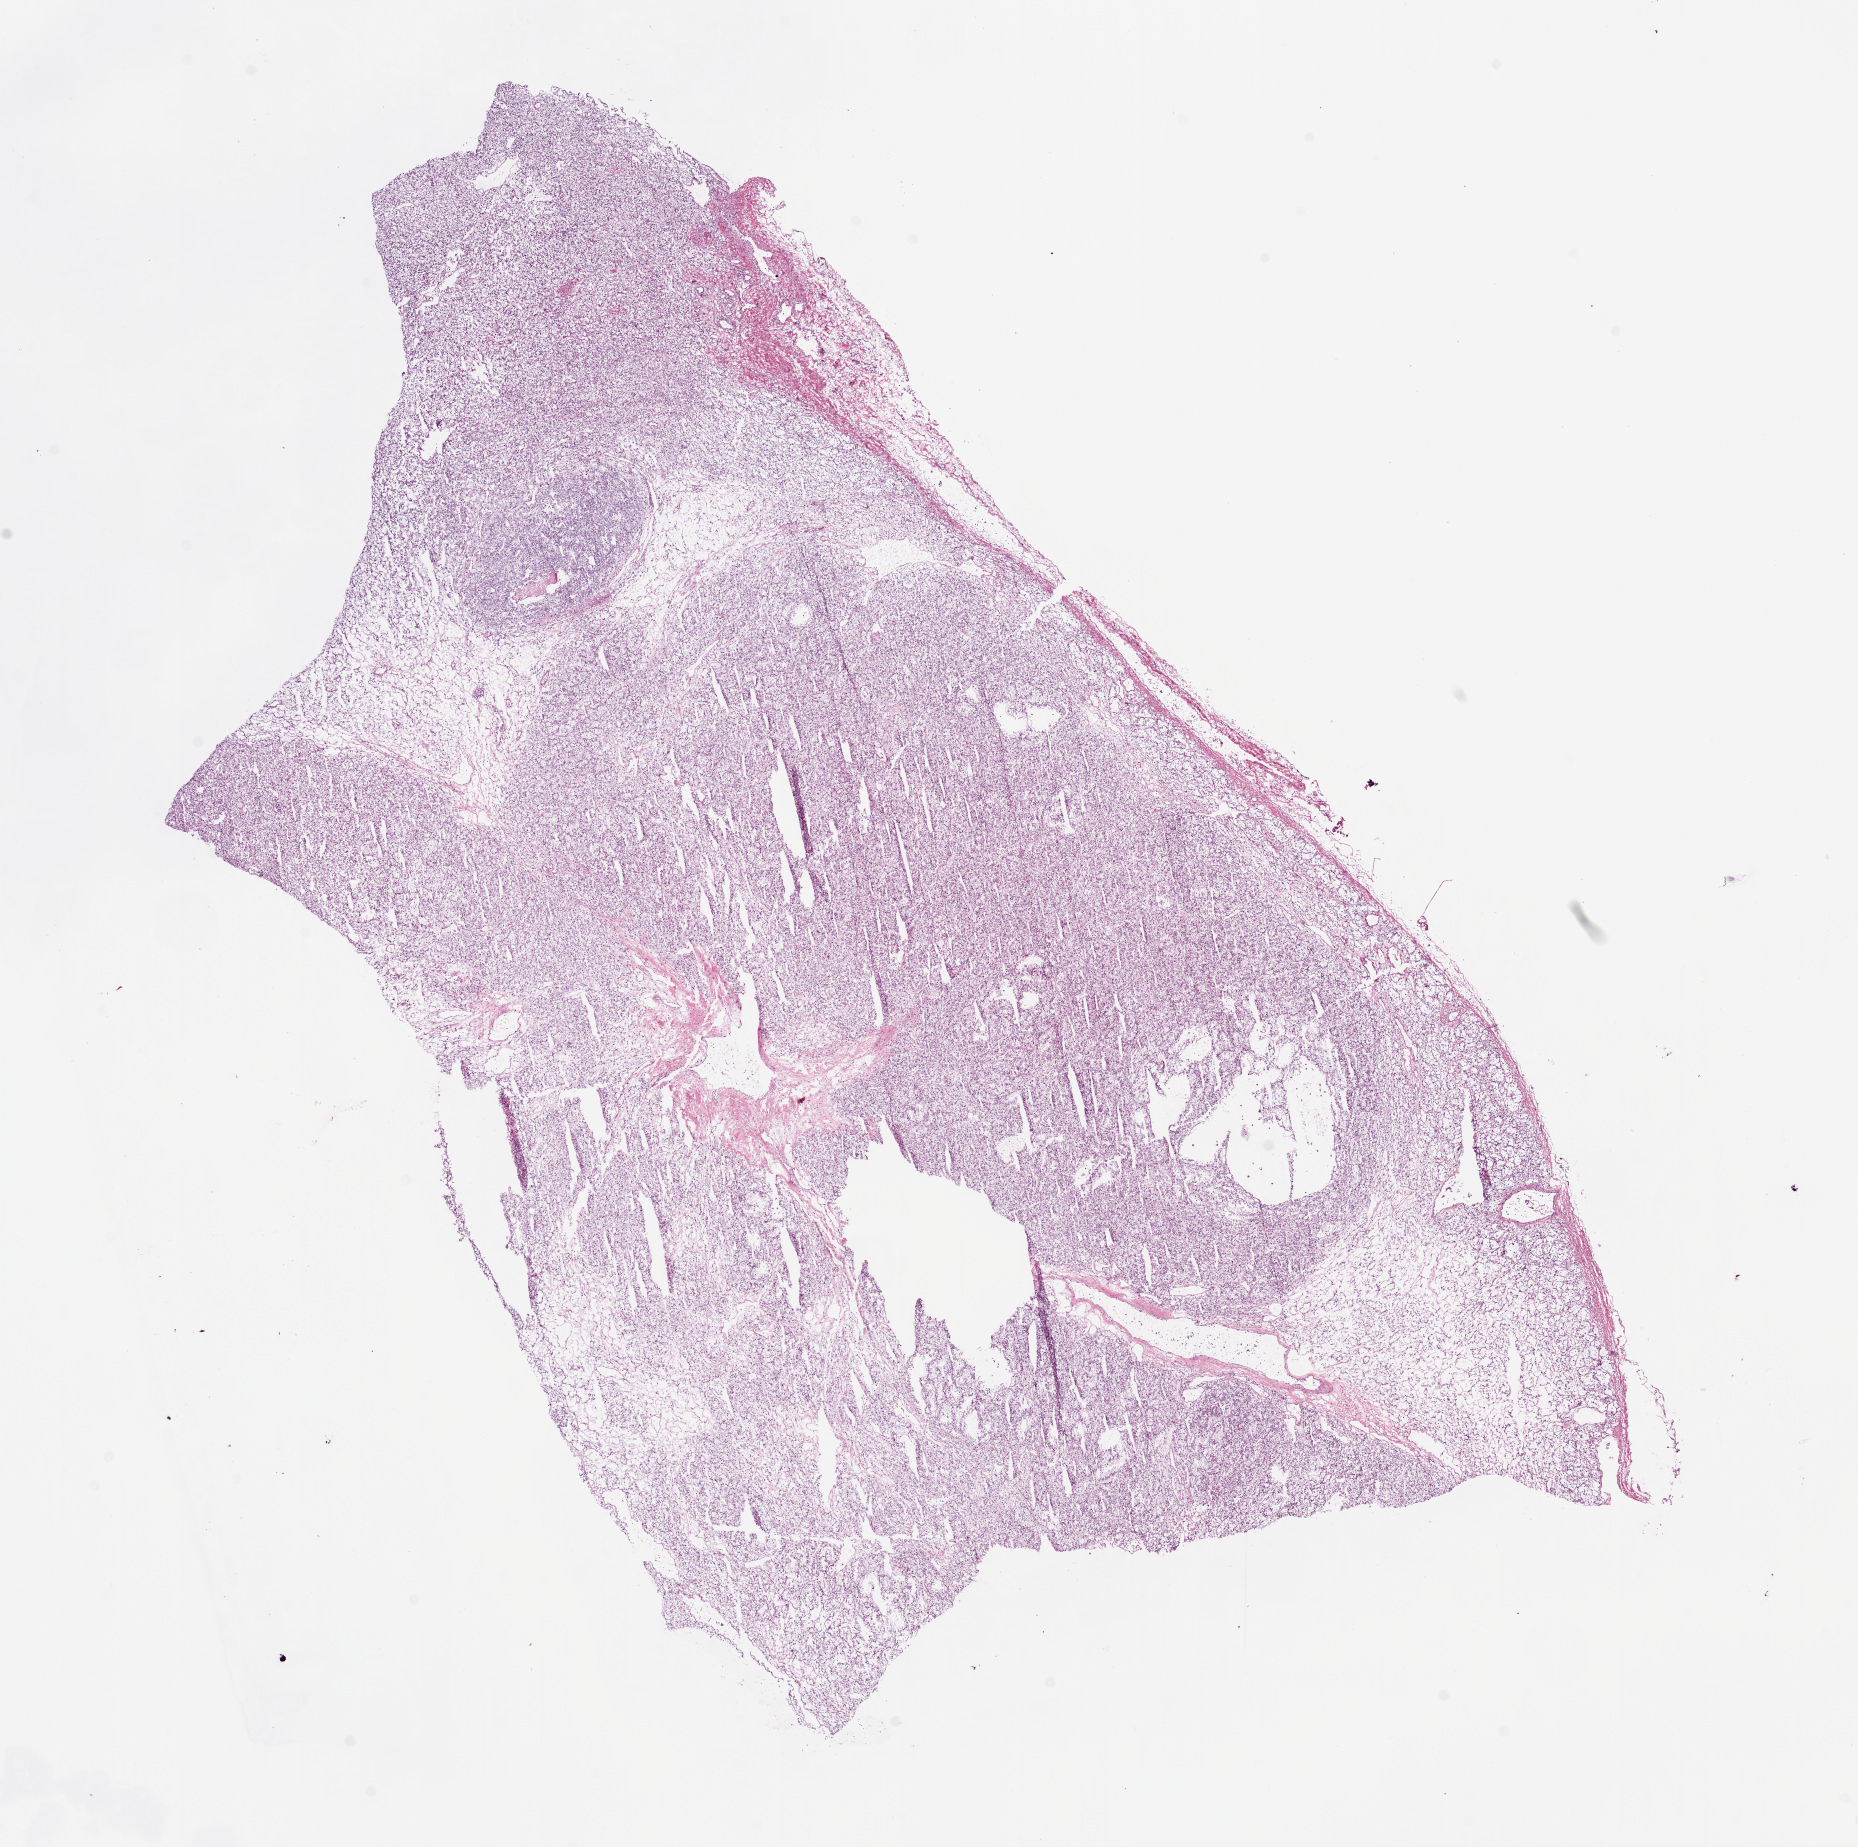
Whole-slide histology image, Hematoxylin and eosin (H&E) stained, low-resolution overview of the scanned area, about 15.0 x 14.9 mm (from a 20x scan); frozen section from the bottom of the tissue portion; kidney, primary tumour sample. Patient: female, age at initial diagnosis 61 years. Histologic grade: G2 (moderately differentiated). Slide review estimates, as recorded: tumour cells 100%, tumour nuclei 90%, normal cells 0%, stromal cells 0%, necrosis 0%. Infiltration values recorded for this section: lymphocyte infiltration 1%, monocyte infiltration 0%, neutrophil infiltration 0%.
Lymph nodes positive (case pathology): 0 of 2 examined. Diagnosis: Clear cell adenocarcinoma, NOS. AJCC pathologic stage: I.